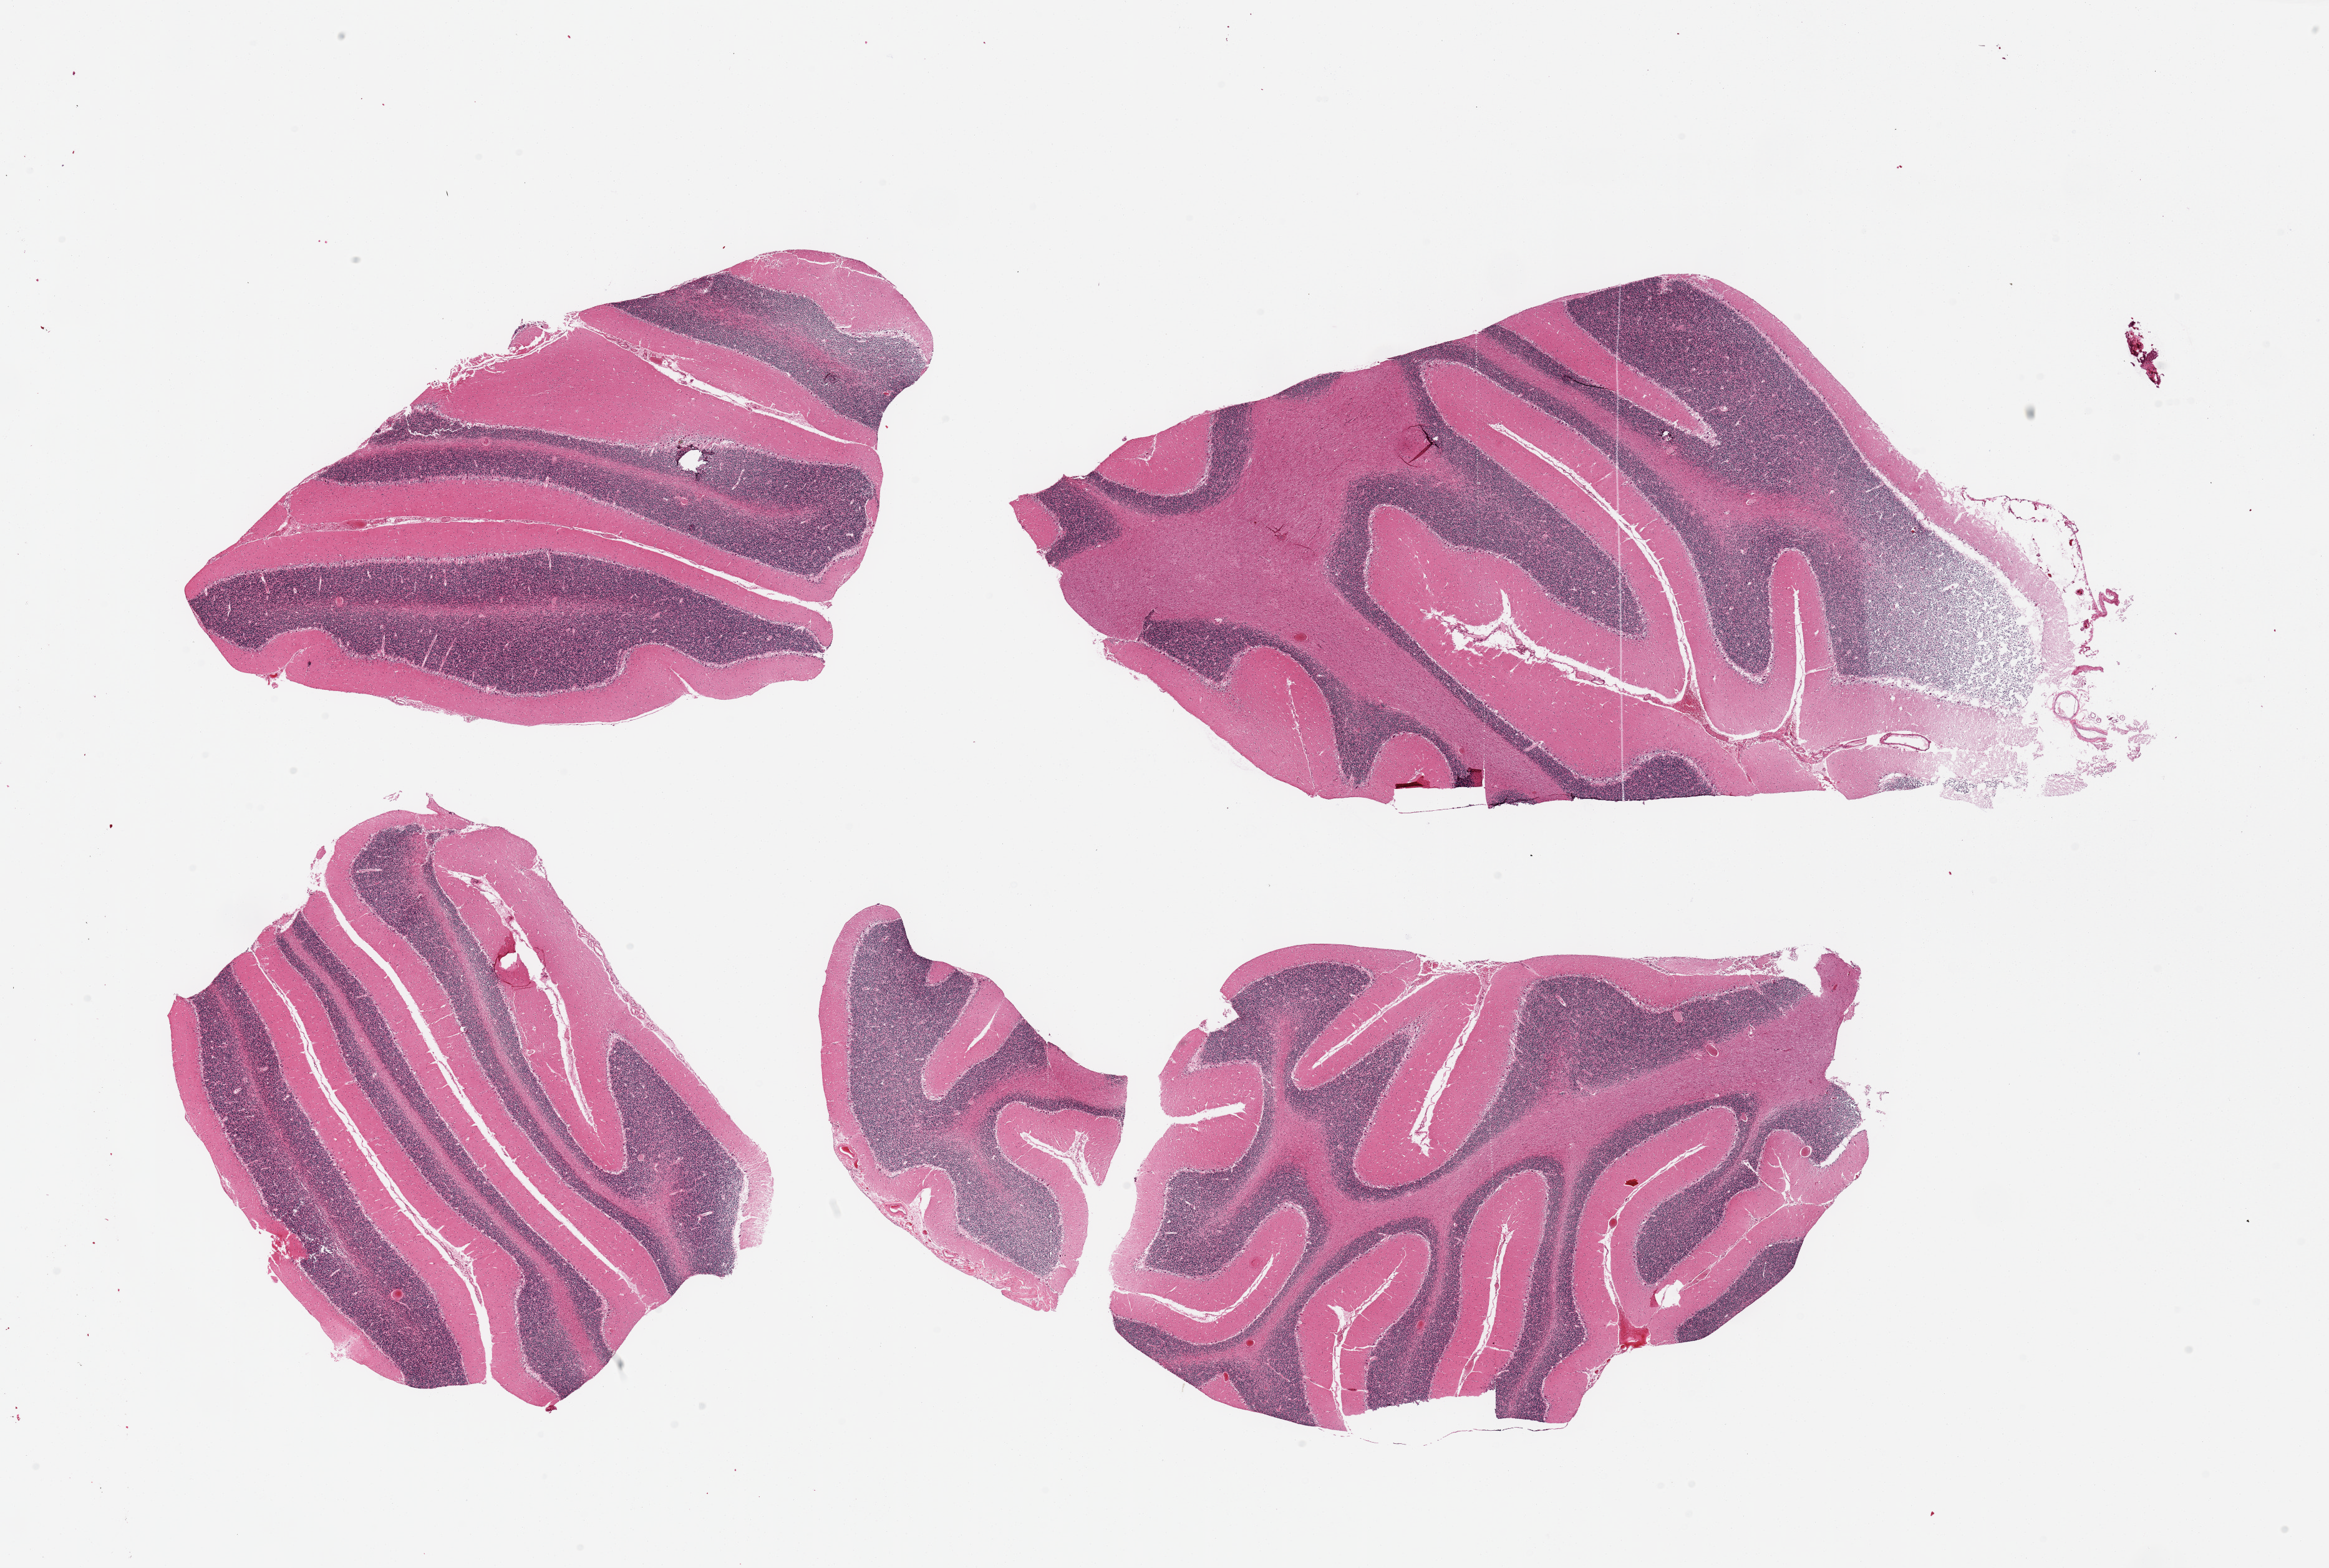
Digitized hematoxylin and eosin (H&E)-stained section, shown as a low-resolution overview of the whole scanned area (about 29.5 x 19.9 mm). PAXgene-fixed paraffin-embedded (PFPE) section. Sampled site (target tissue): cerebellum. Donor tissue sample. Donor: male.
Reviewer comment on this tissue sample: 5 pieces; mild to moderate autolysis; focus of attached meninges; Purkinje cells present.